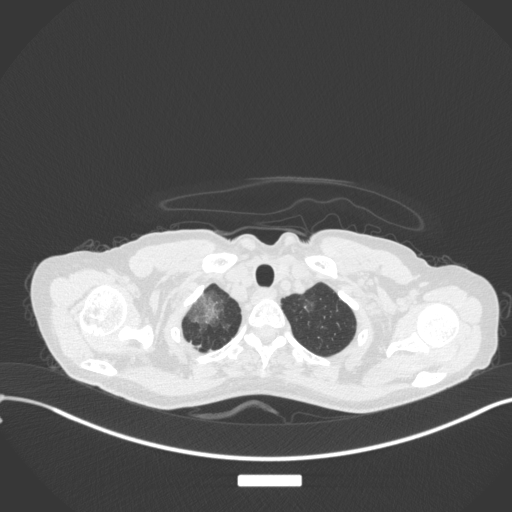
Chest CT, one axial slice. Slice 304 of 311 in the series (ordered by position). Reconstruction kernel B31f. 120 kVp. Lung window (W 1500 / L -600 HU). 1 mm slice thickness. 512 × 512 image matrix, field of view 400 × 400 mm. Female patient, age 59 years. From the clinical record (not read from this slice): clinical TNM (as recorded): T3 N0 M0; histopathological grade: G1.
Structures marked on this image (rectangle marked by the reading radiologist):
- lung tumour (recorded histology: adenocarcinoma): bounding box [x1, y1, x2, y2] px = [185, 295, 221, 327]